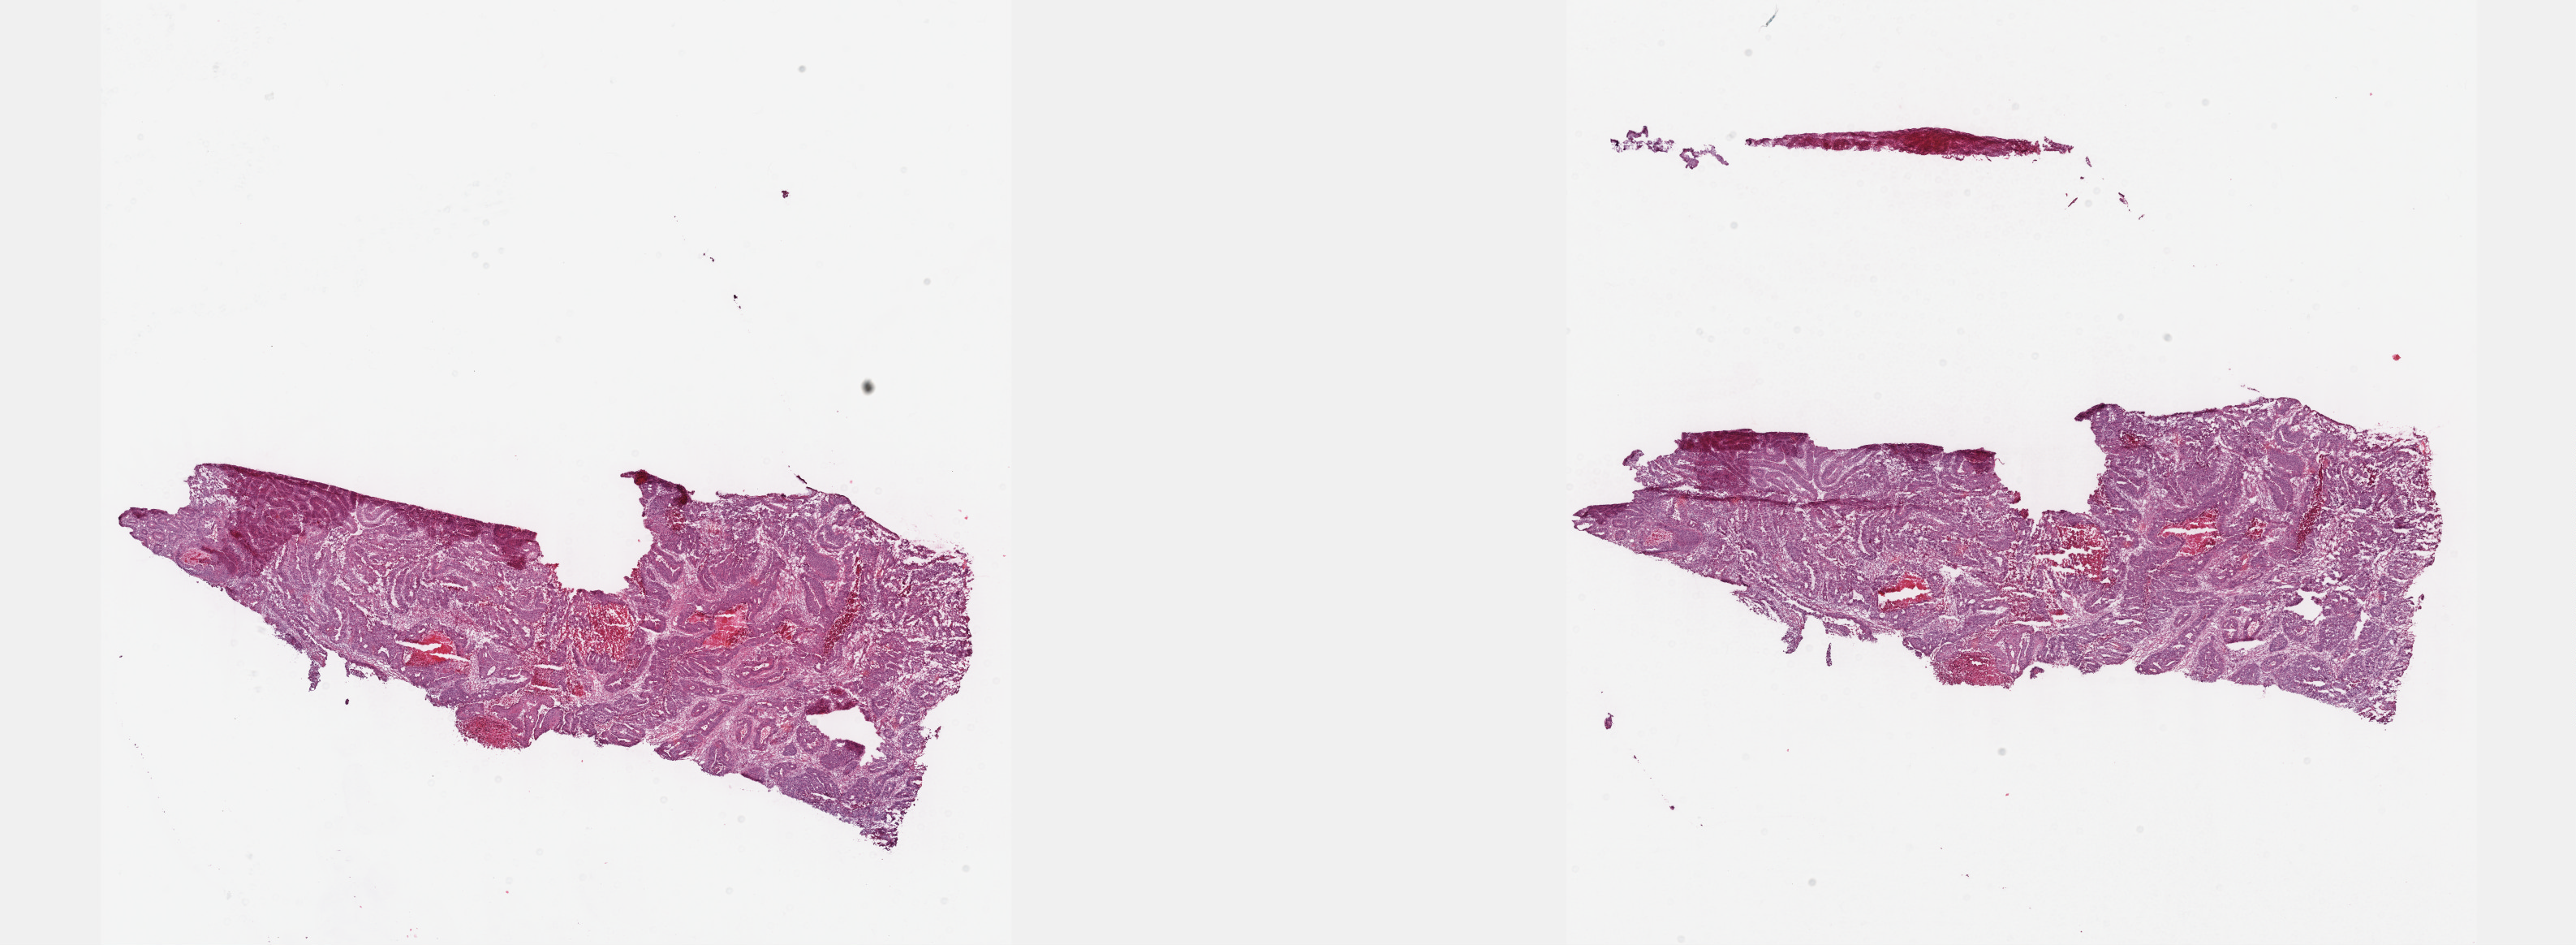
Digitized H&E-stained tissue section (whole slide) — shown as a low-resolution overview of the whole scanned area (about 25.7 x 9.4 mm); frozen section from the bottom of the tissue portion; sample: primary tumour, colon. Female patient; age at initial diagnosis 82 years. Composition of this section per pathologist review: tumour cells 77%, tumour nuclei 80%, normal cells 5%, stromal cells 8%, necrosis 10%. Infiltration values recorded for this section: lymphocyte infiltration 5%, monocyte infiltration 1%, neutrophil infiltration 2%.
Diagnosis: Adenocarcinoma, NOS (cecum). Lymph nodes positive (case pathology): 4 of 16 examined. AJCC pathologic stage: IV (6th edition).